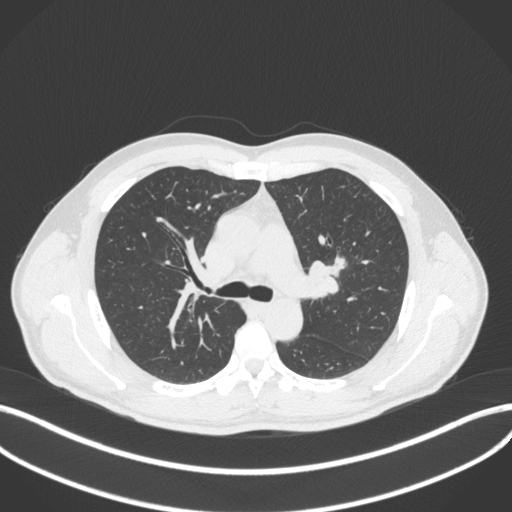
Chest CT, one axial slice; position 275 of 383 along the scan axis; lung window (W 1500 / L -600 HU); 1 mm slice thickness; 512 × 512 image matrix. Male patient, age 50 years. Case-level facts recorded for this patient, not image findings: clinical TNM (as recorded): T1c N1 M1b.
Annotated regions visible in this slice (bounding box drawn by a radiologist):
- lung tumour (recorded histology: squamous cell carcinoma): bounding box [x1, y1, x2, y2] px = [311, 248, 349, 302]